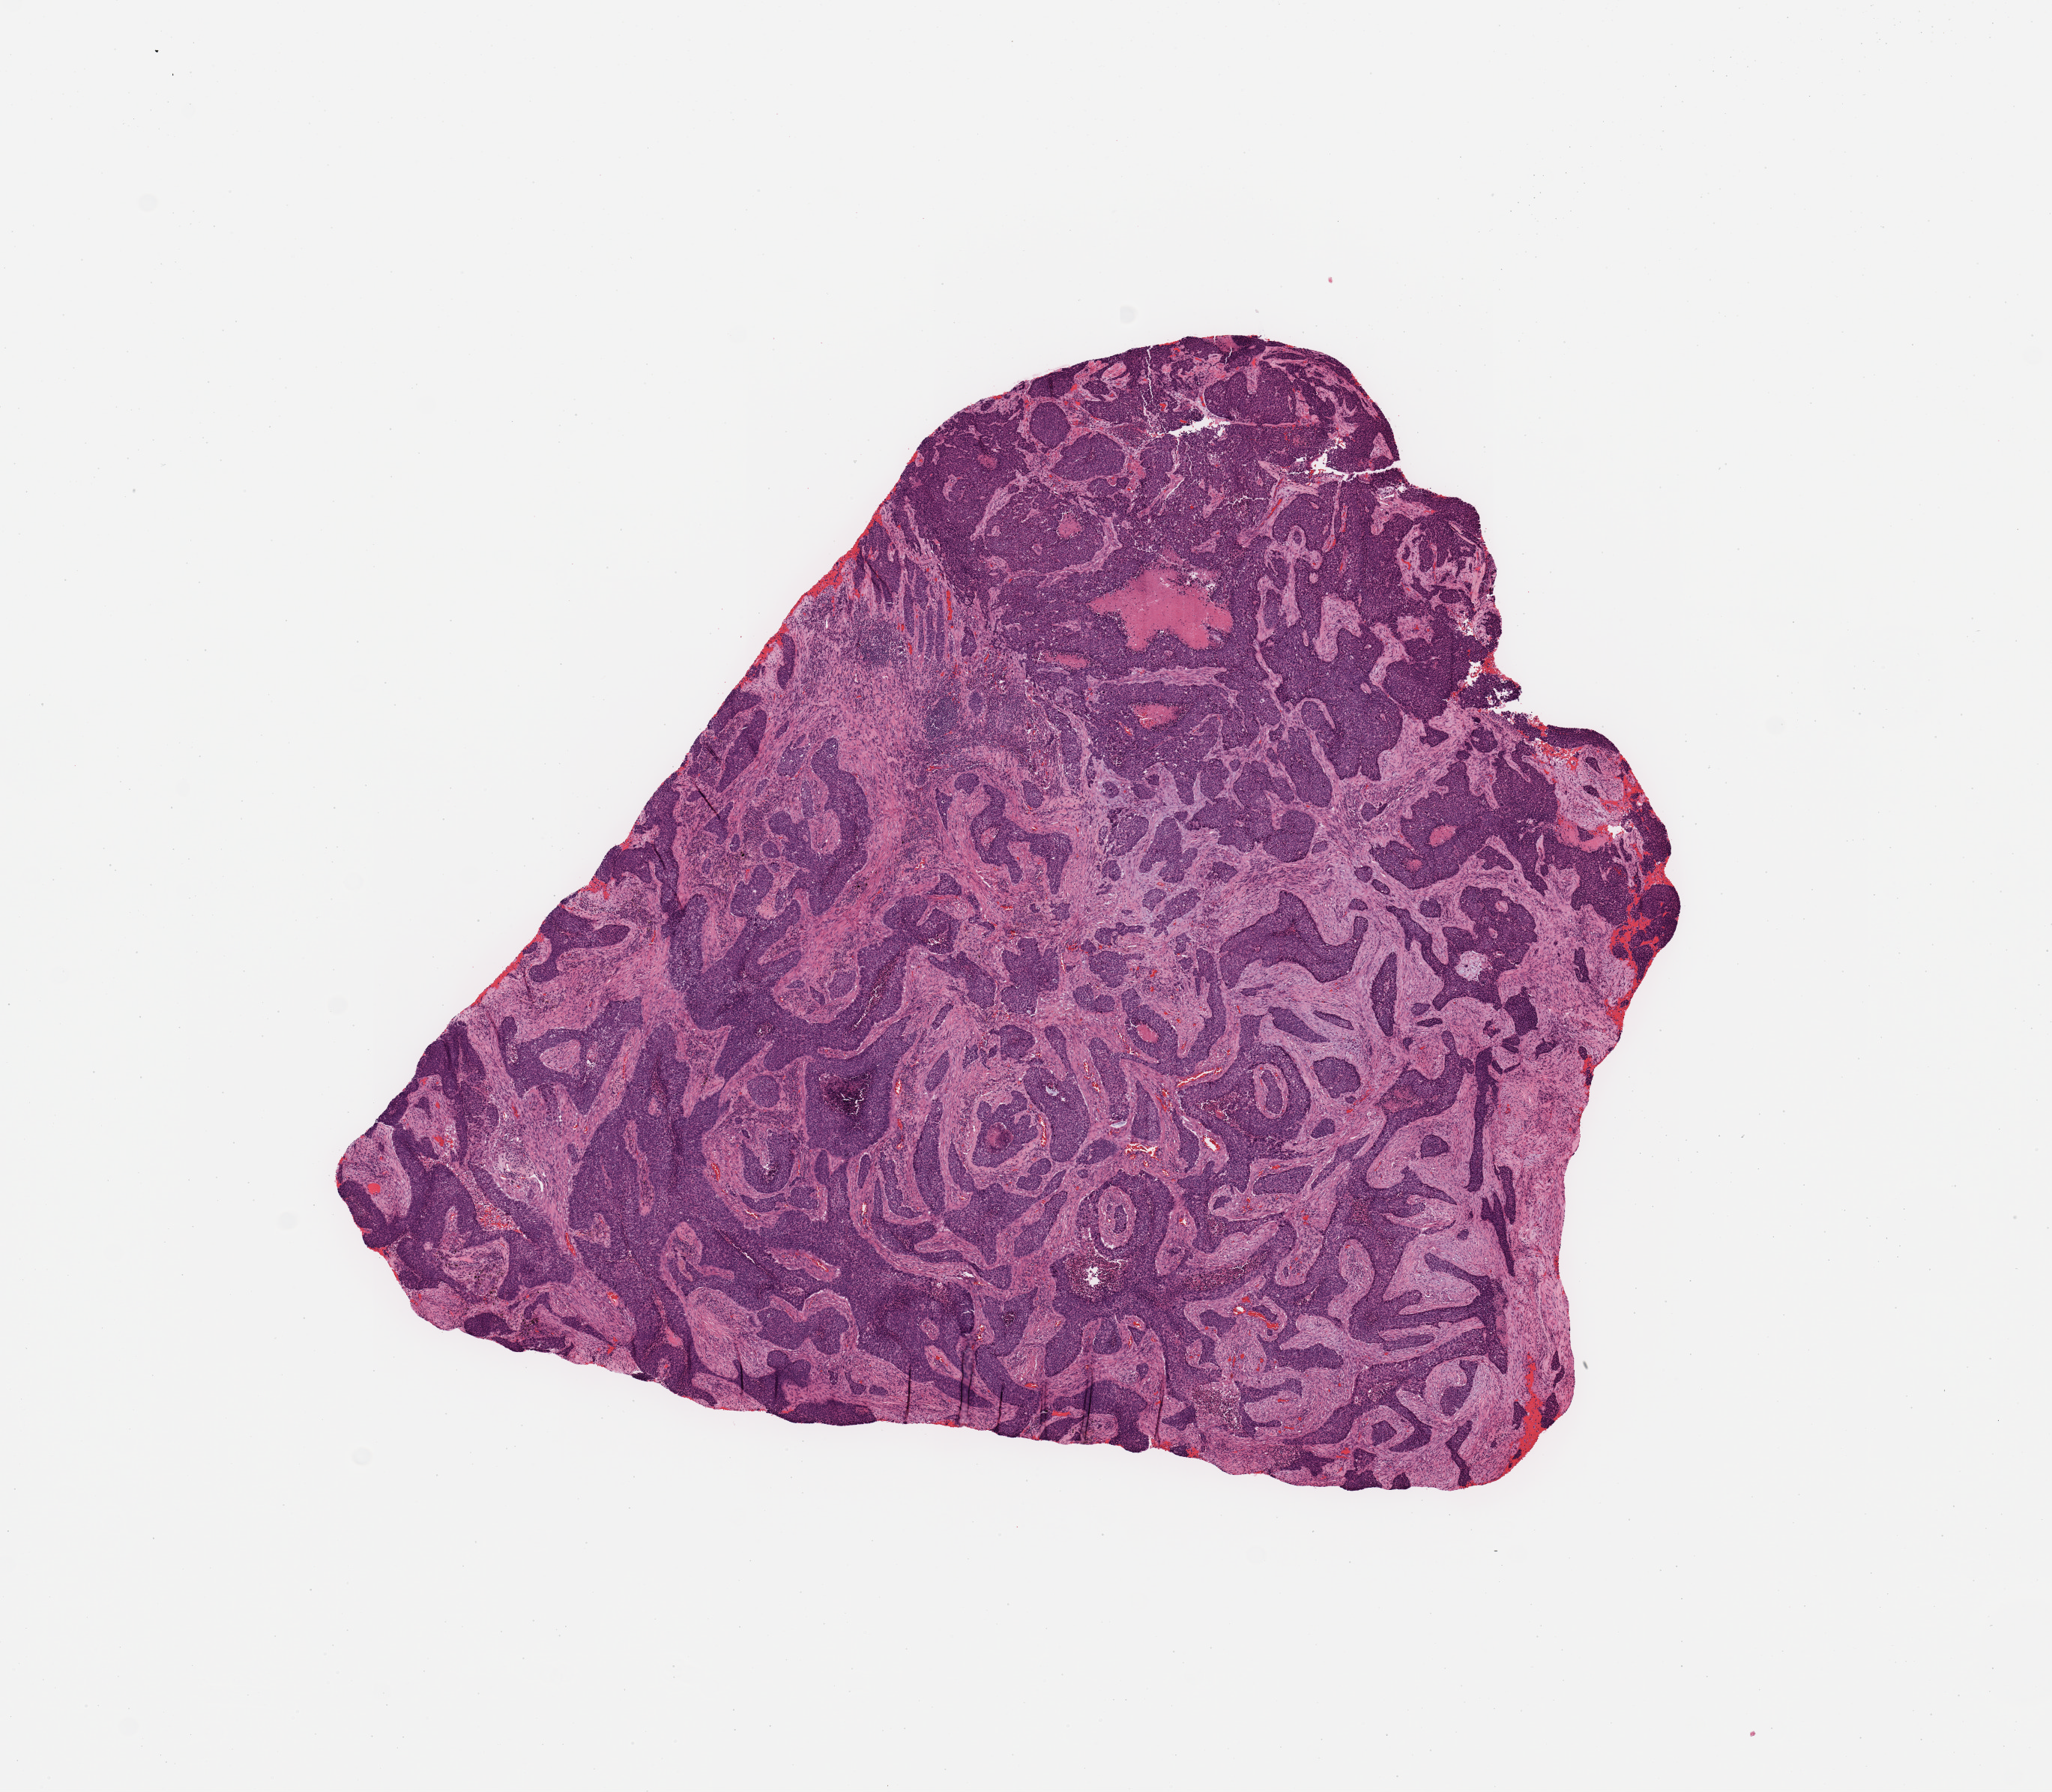
H&E whole-slide image — whole scanned area (about 10.8 x 9.5 mm, slide scanned at 20x) shown as a low-resolution overview; tumour tissue sample, sampled site: lung. 54-year-old male patient. Histologic grade: G2 (moderately differentiated). Composition of this section per pathologist review: tumour nuclei 65%, necrosis 5%.
• primary tumour site (as recorded): left upper lobe
• AJCC pathologic stage: IIA
• diagnosis: Squamous cell carcinoma, NOS